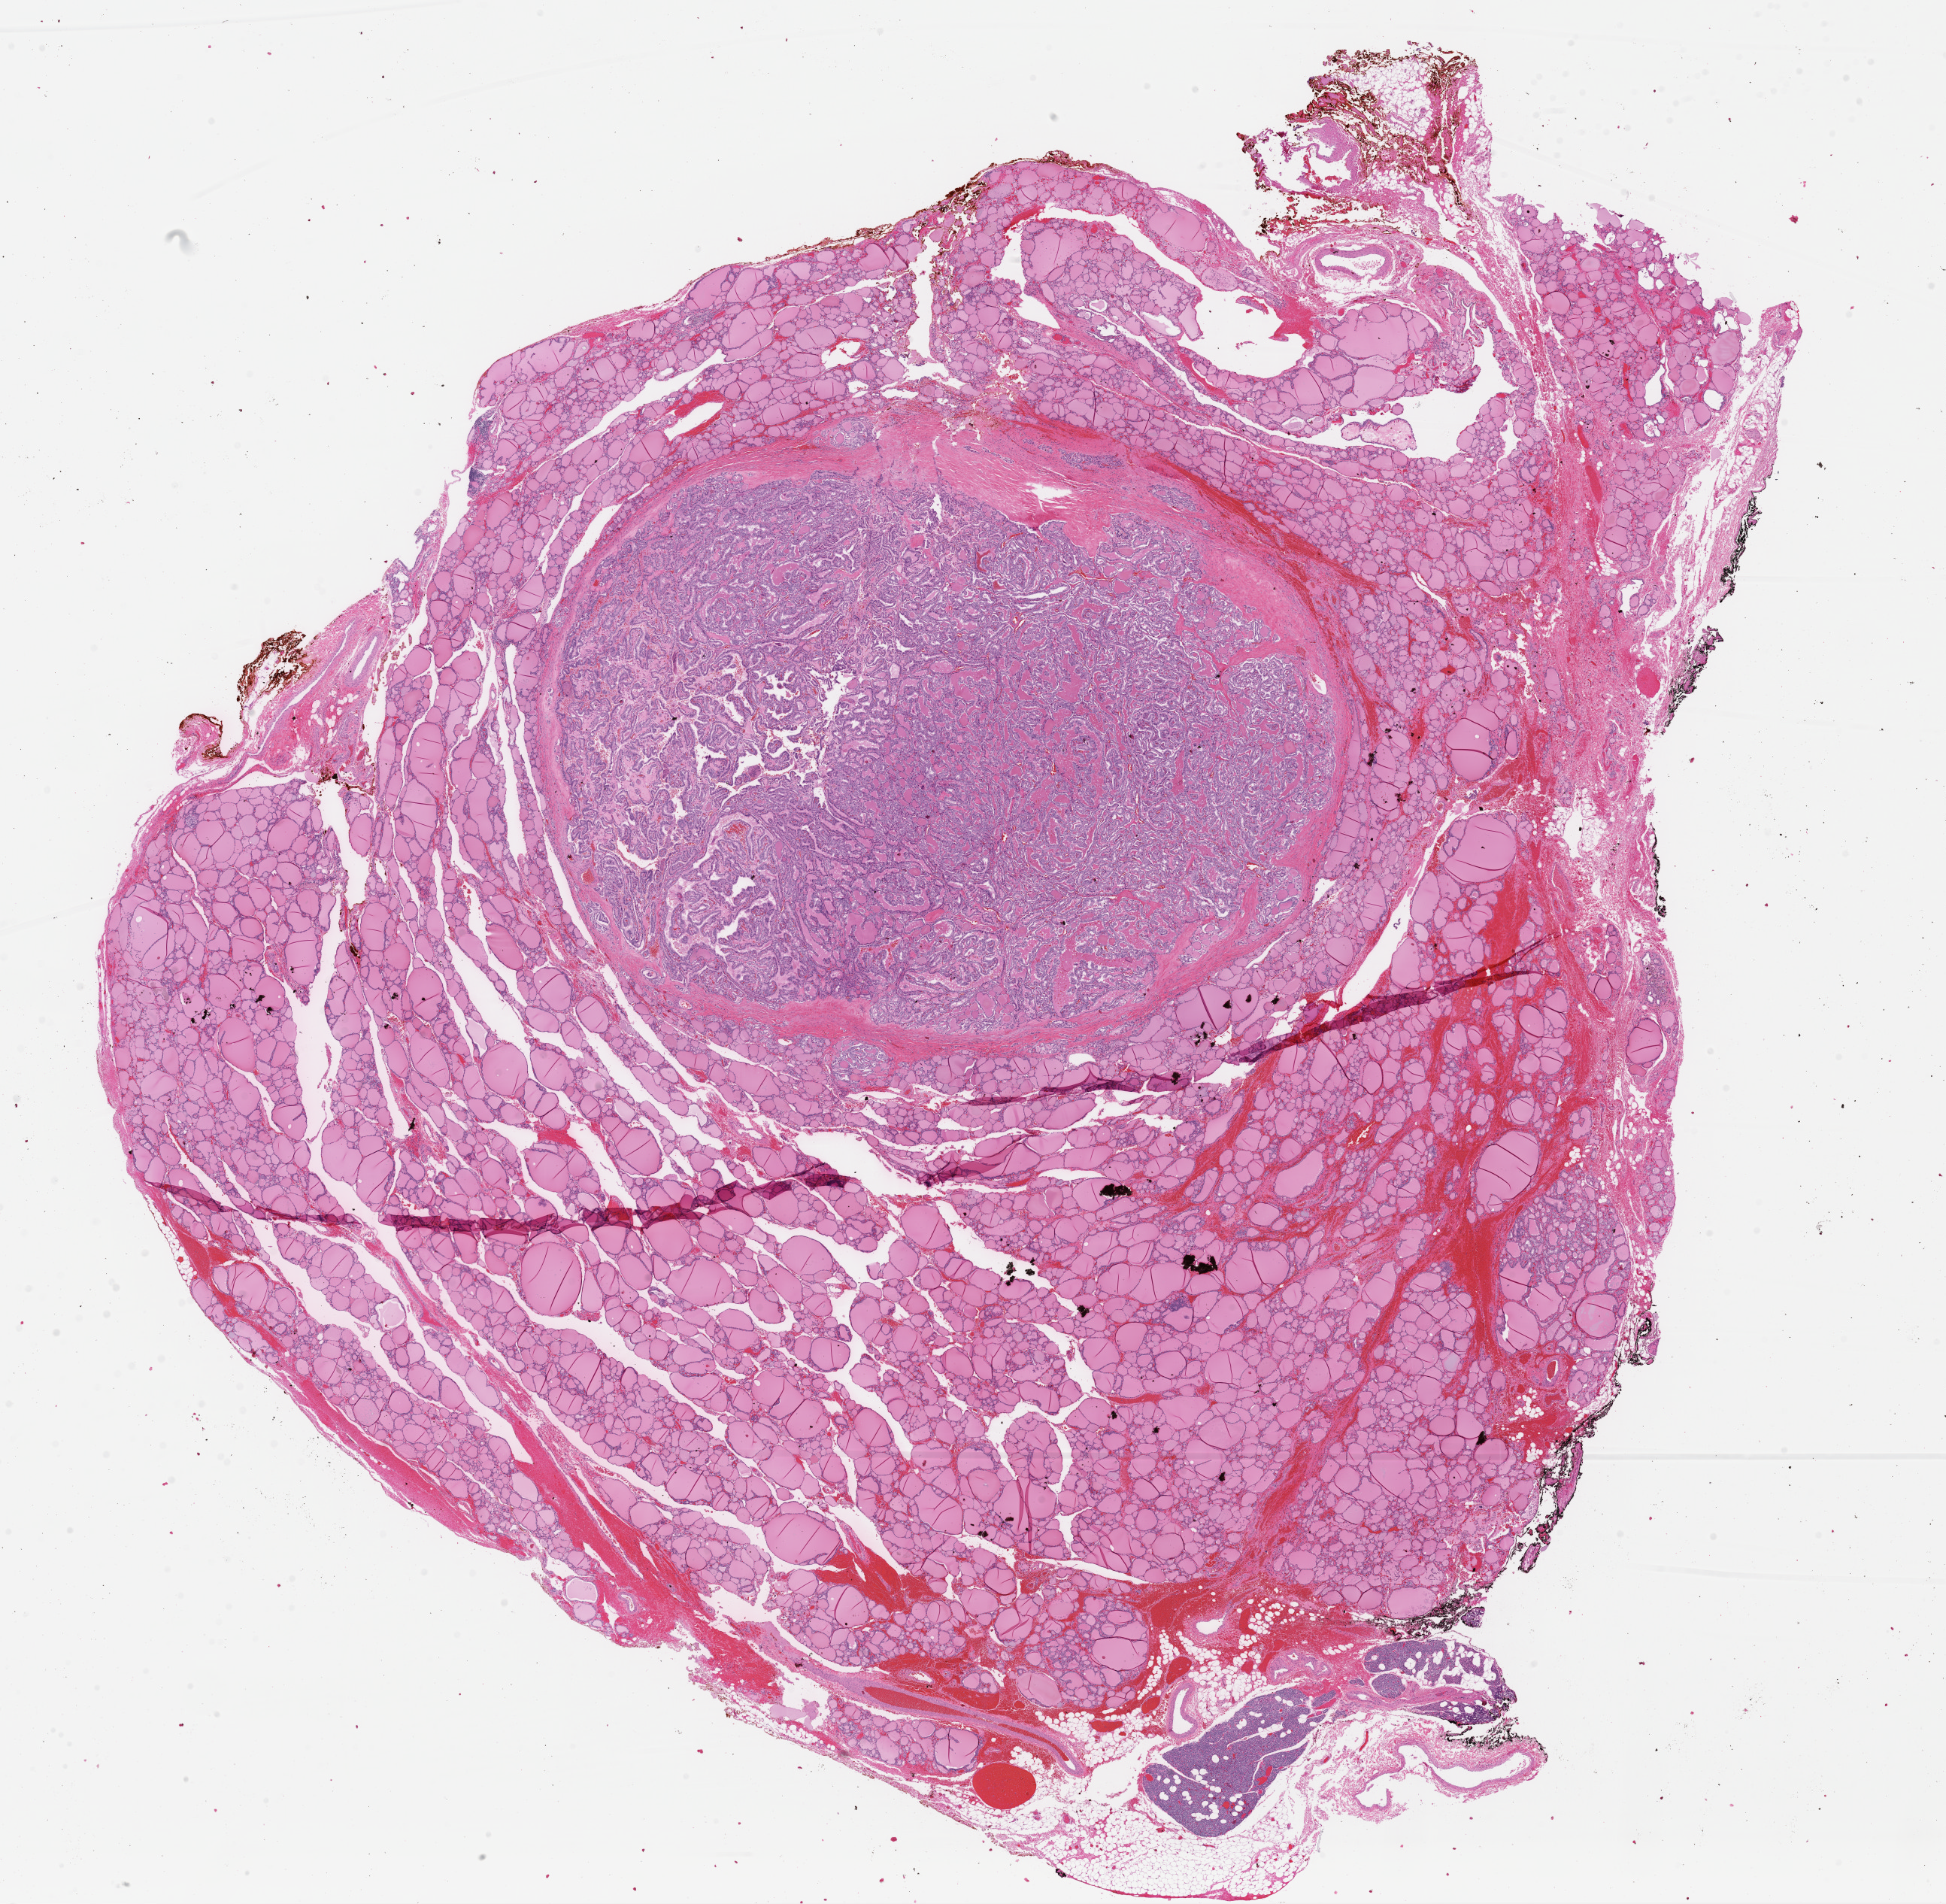
Whole-slide histology image, H&E-stained — low-resolution overview of the scanned area, about 20.4 x 20.0 mm; FFPE section; thyroid, primary tumour sample. Male, age 39 years at initial diagnosis.
• laterality: right
• lymph nodes positive (case pathology): 0 of 6 examined
• AJCC pathologic stage: I (7th edition)
• diagnosis: Papillary adenocarcinoma, NOS (thyroid gland)